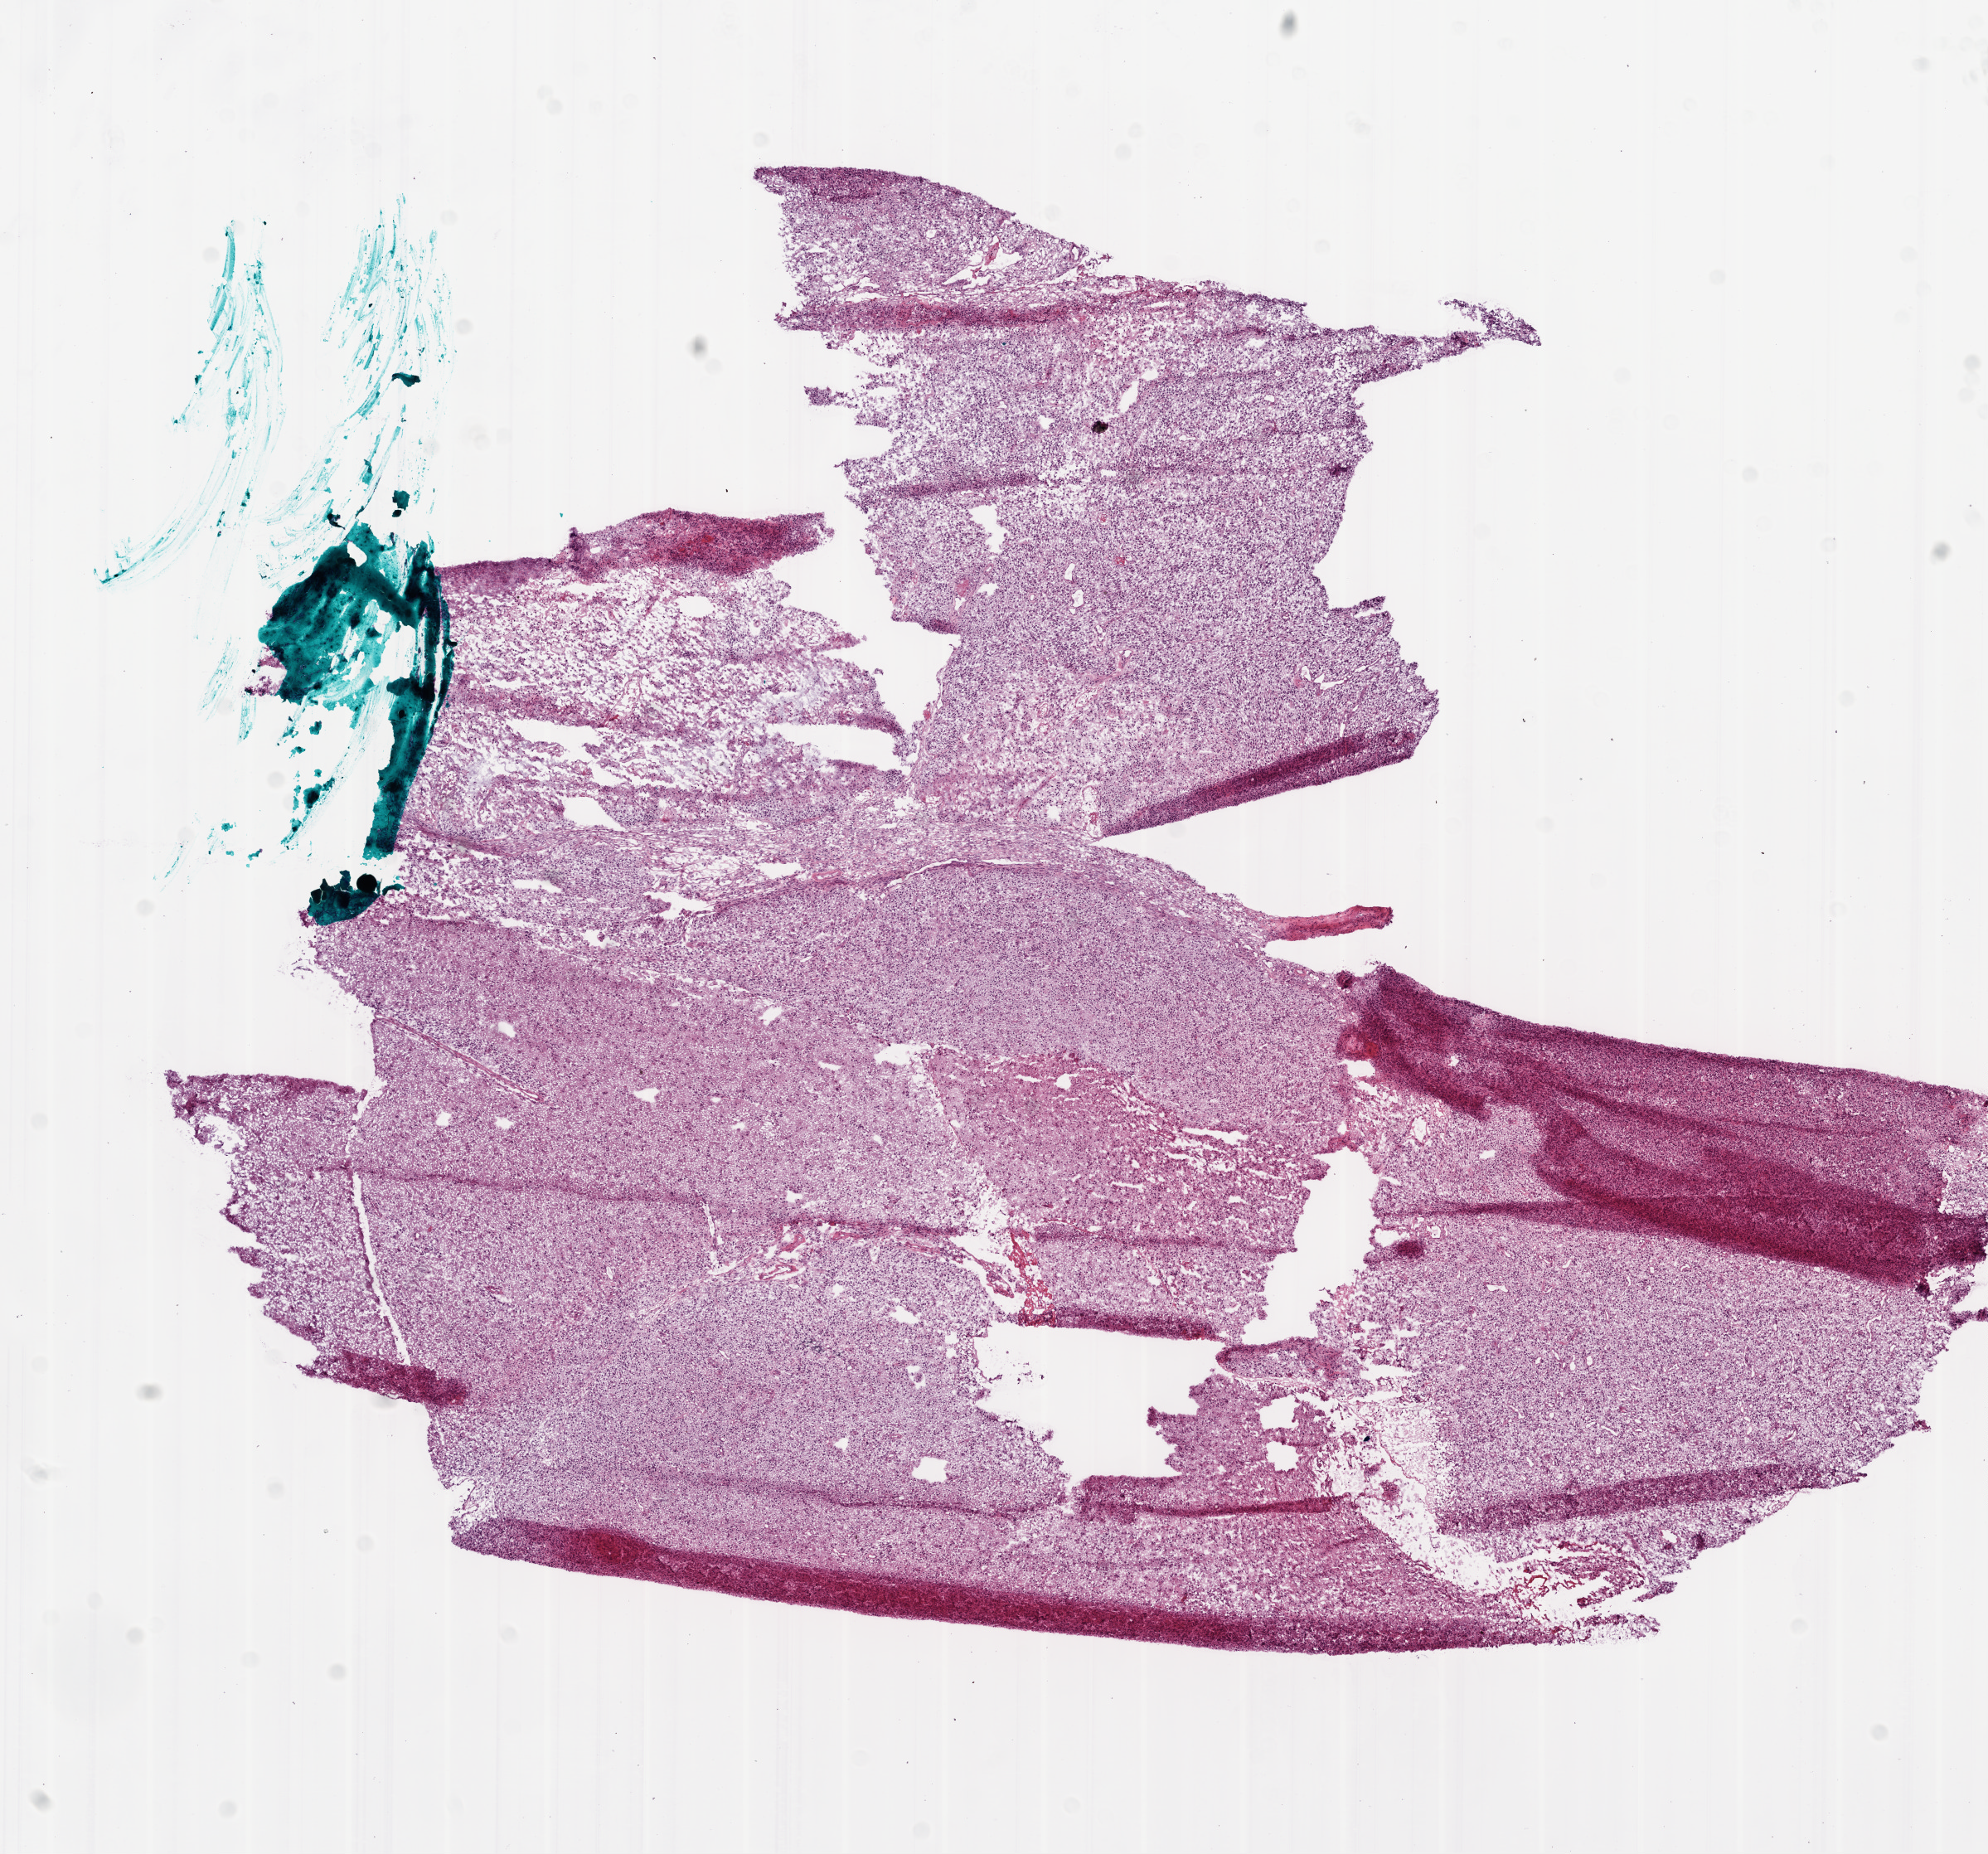
Digitized H&E tissue section (whole slide) — a low-resolution overview of the entire scanned area, about 9.7 x 9.0 mm; frozen section; brain, primary tumour sample. Male, age 69 years at initial diagnosis. Slide review estimates, as recorded: tumour cells 75%, tumour nuclei 95%, normal cells 0%, stromal cells 10%, necrosis 15%.
Pathologic diagnosis: Glioblastoma.